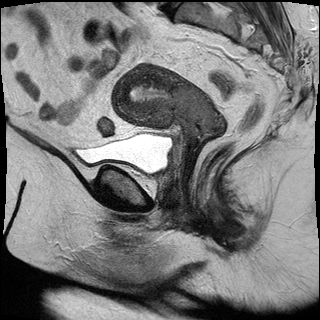
Pelvic MRI for cervical cancer, one sagittal slice. Position 13 of 30 along the scan axis. T2-weighted. 1.5 T. TE 89 ms, TR 2930 ms. 4 mm slice thickness. 320 × 320 image matrix, field of view 260 × 260 mm. Female patient, age 53 years.
Outlined on this slice (manually delineated by an expert):
- uterus and cervix: box from (x=111, y=63) to (x=226, y=150) px